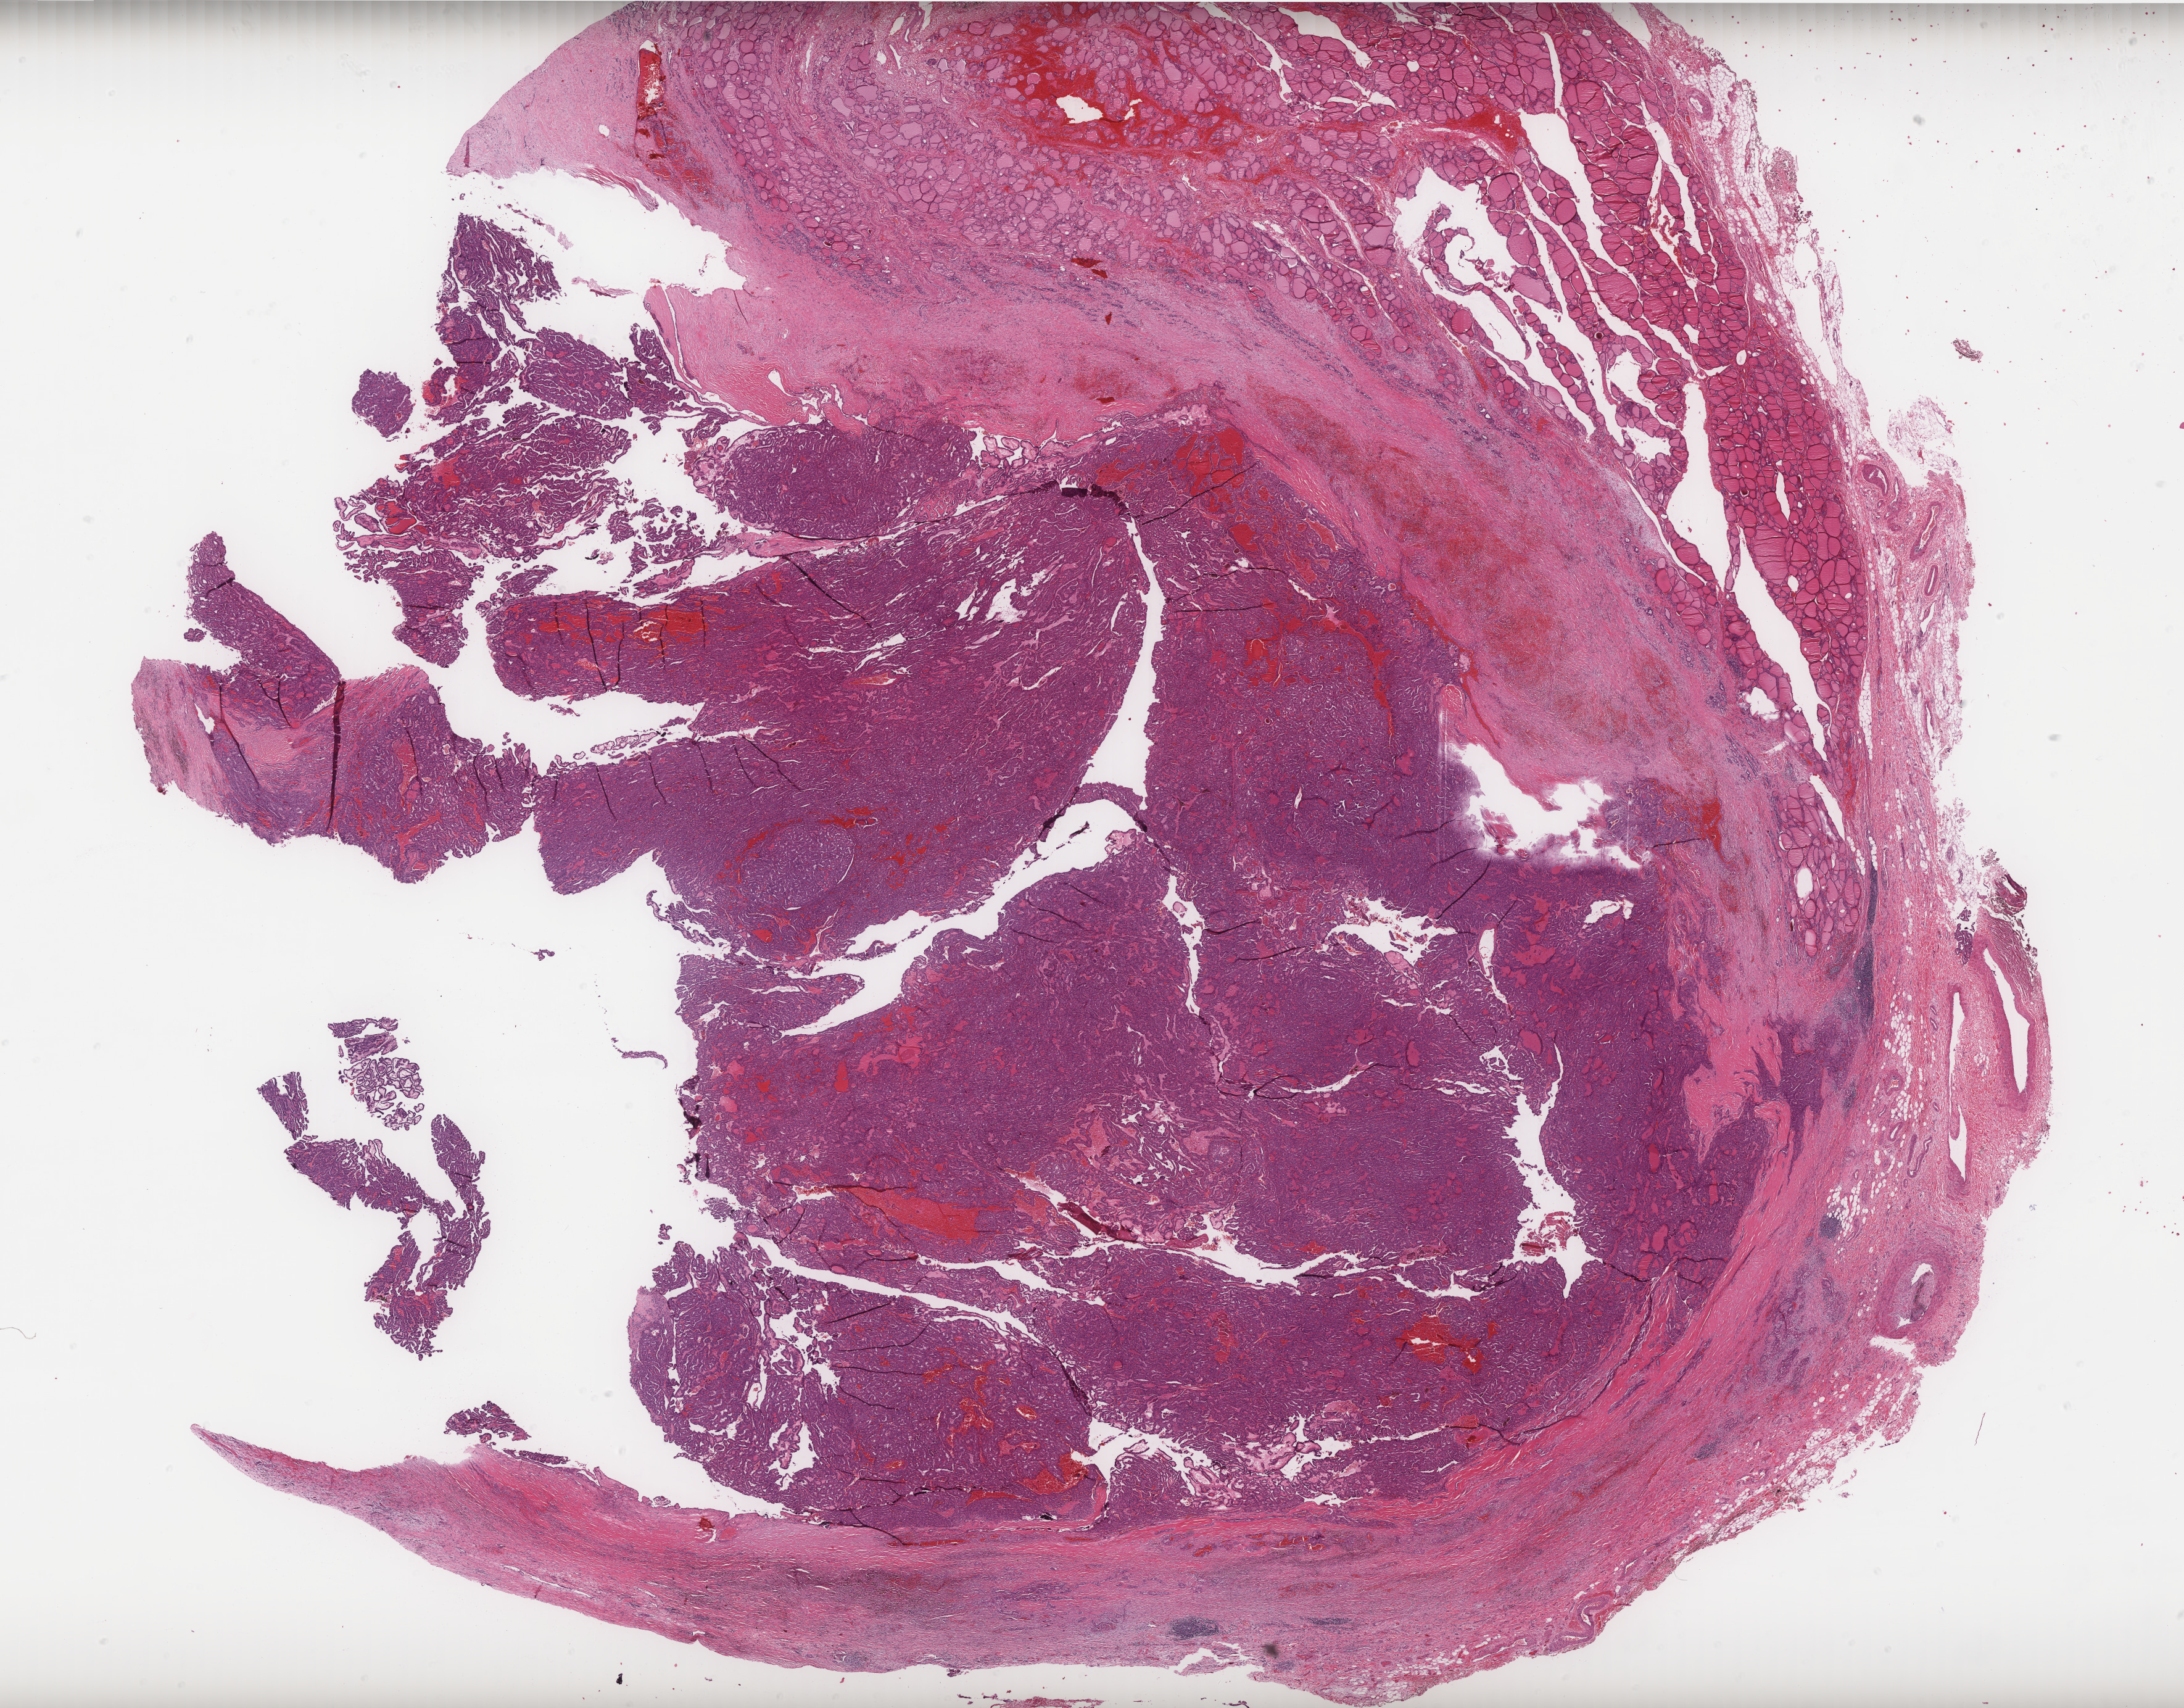
Whole-slide histology image, H&E-stained — shown as a low-resolution overview of the whole scanned area (about 28.4 x 22.2 mm, slide scanned at 40x). FFPE section. Thyroid, primary tumour sample. Patient: male, age at initial diagnosis 58 years.
Pathologic diagnosis: Papillary adenocarcinoma, NOS (thyroid gland).